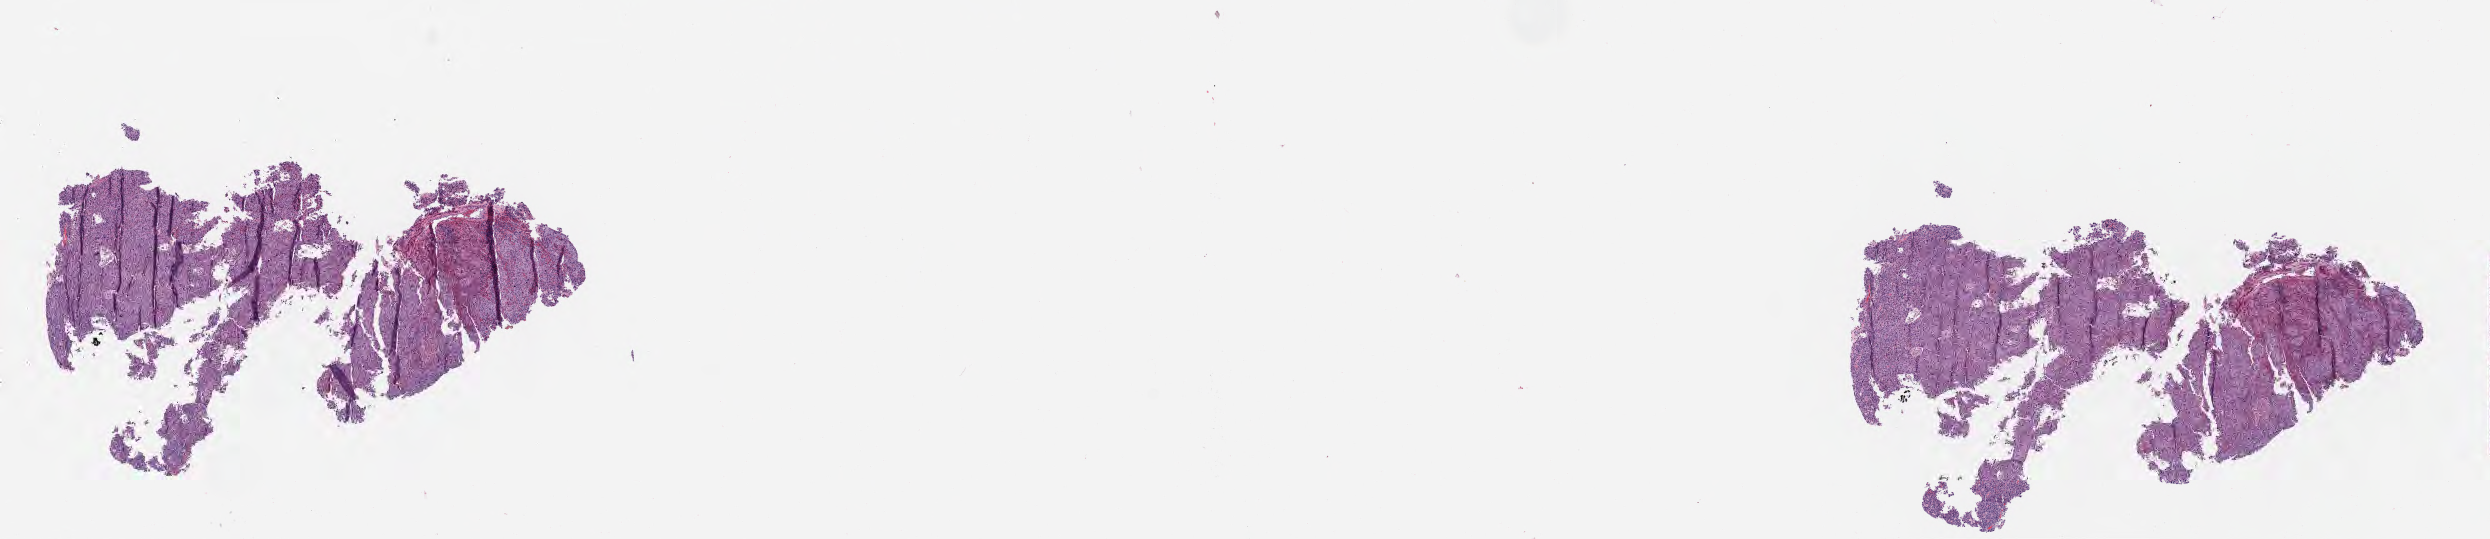
Whole-slide image, hematoxylin and eosin (H&E) stain — low-resolution overview of the scanned area, about 20.1 x 4.4 mm, tumor tissue, site: cervix. Patient: female, 39 years old.
Histologic diagnosis: Squamous cell carcinoma, large cell, nonkeratinizing, NOS.